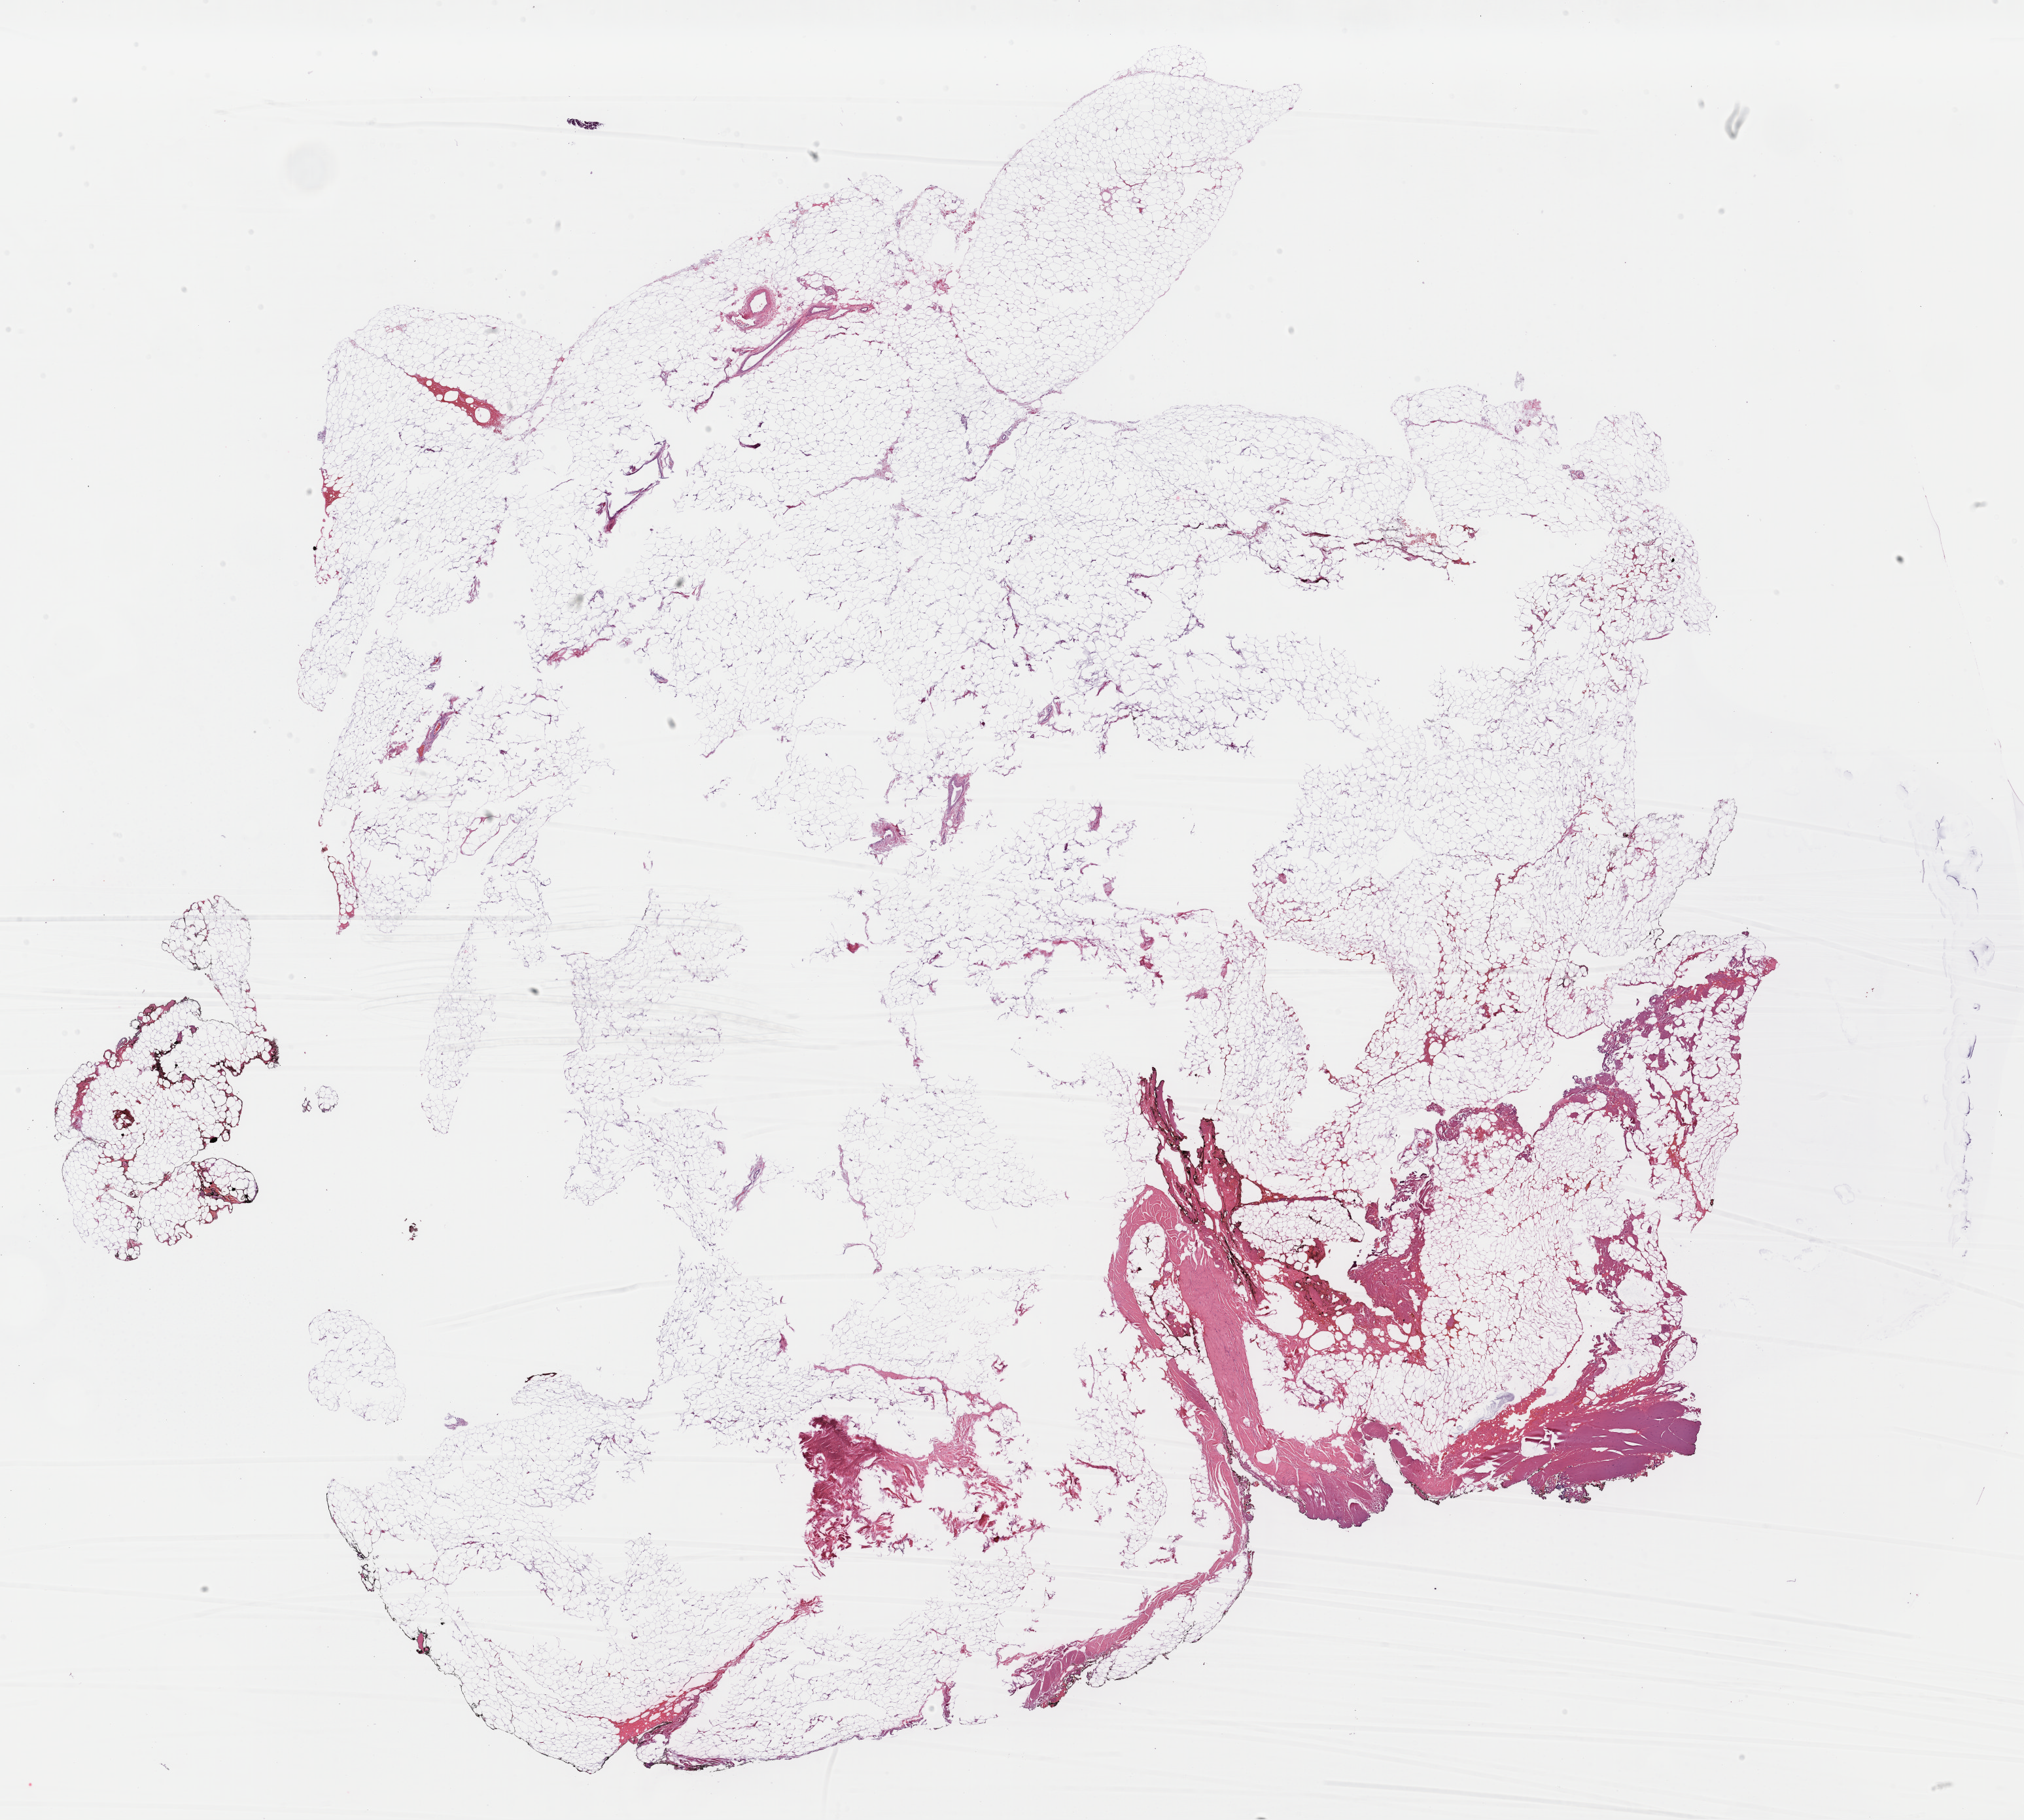
H&E whole-slide image, shown as a low-resolution overview of the whole scanned area (about 24.4 x 22.0 mm), formalin-fixed paraffin-embedded (FFPE) diagnostic section, breast, primary tumour sample. Female, age 51 years at initial diagnosis.
- TNM: T2 N0 M0
- diagnosis: Infiltrating duct carcinoma, NOS
- AJCC pathologic stage: IIA (7th edition)
- lymph nodes positive (case pathology): 0 of 5 examined